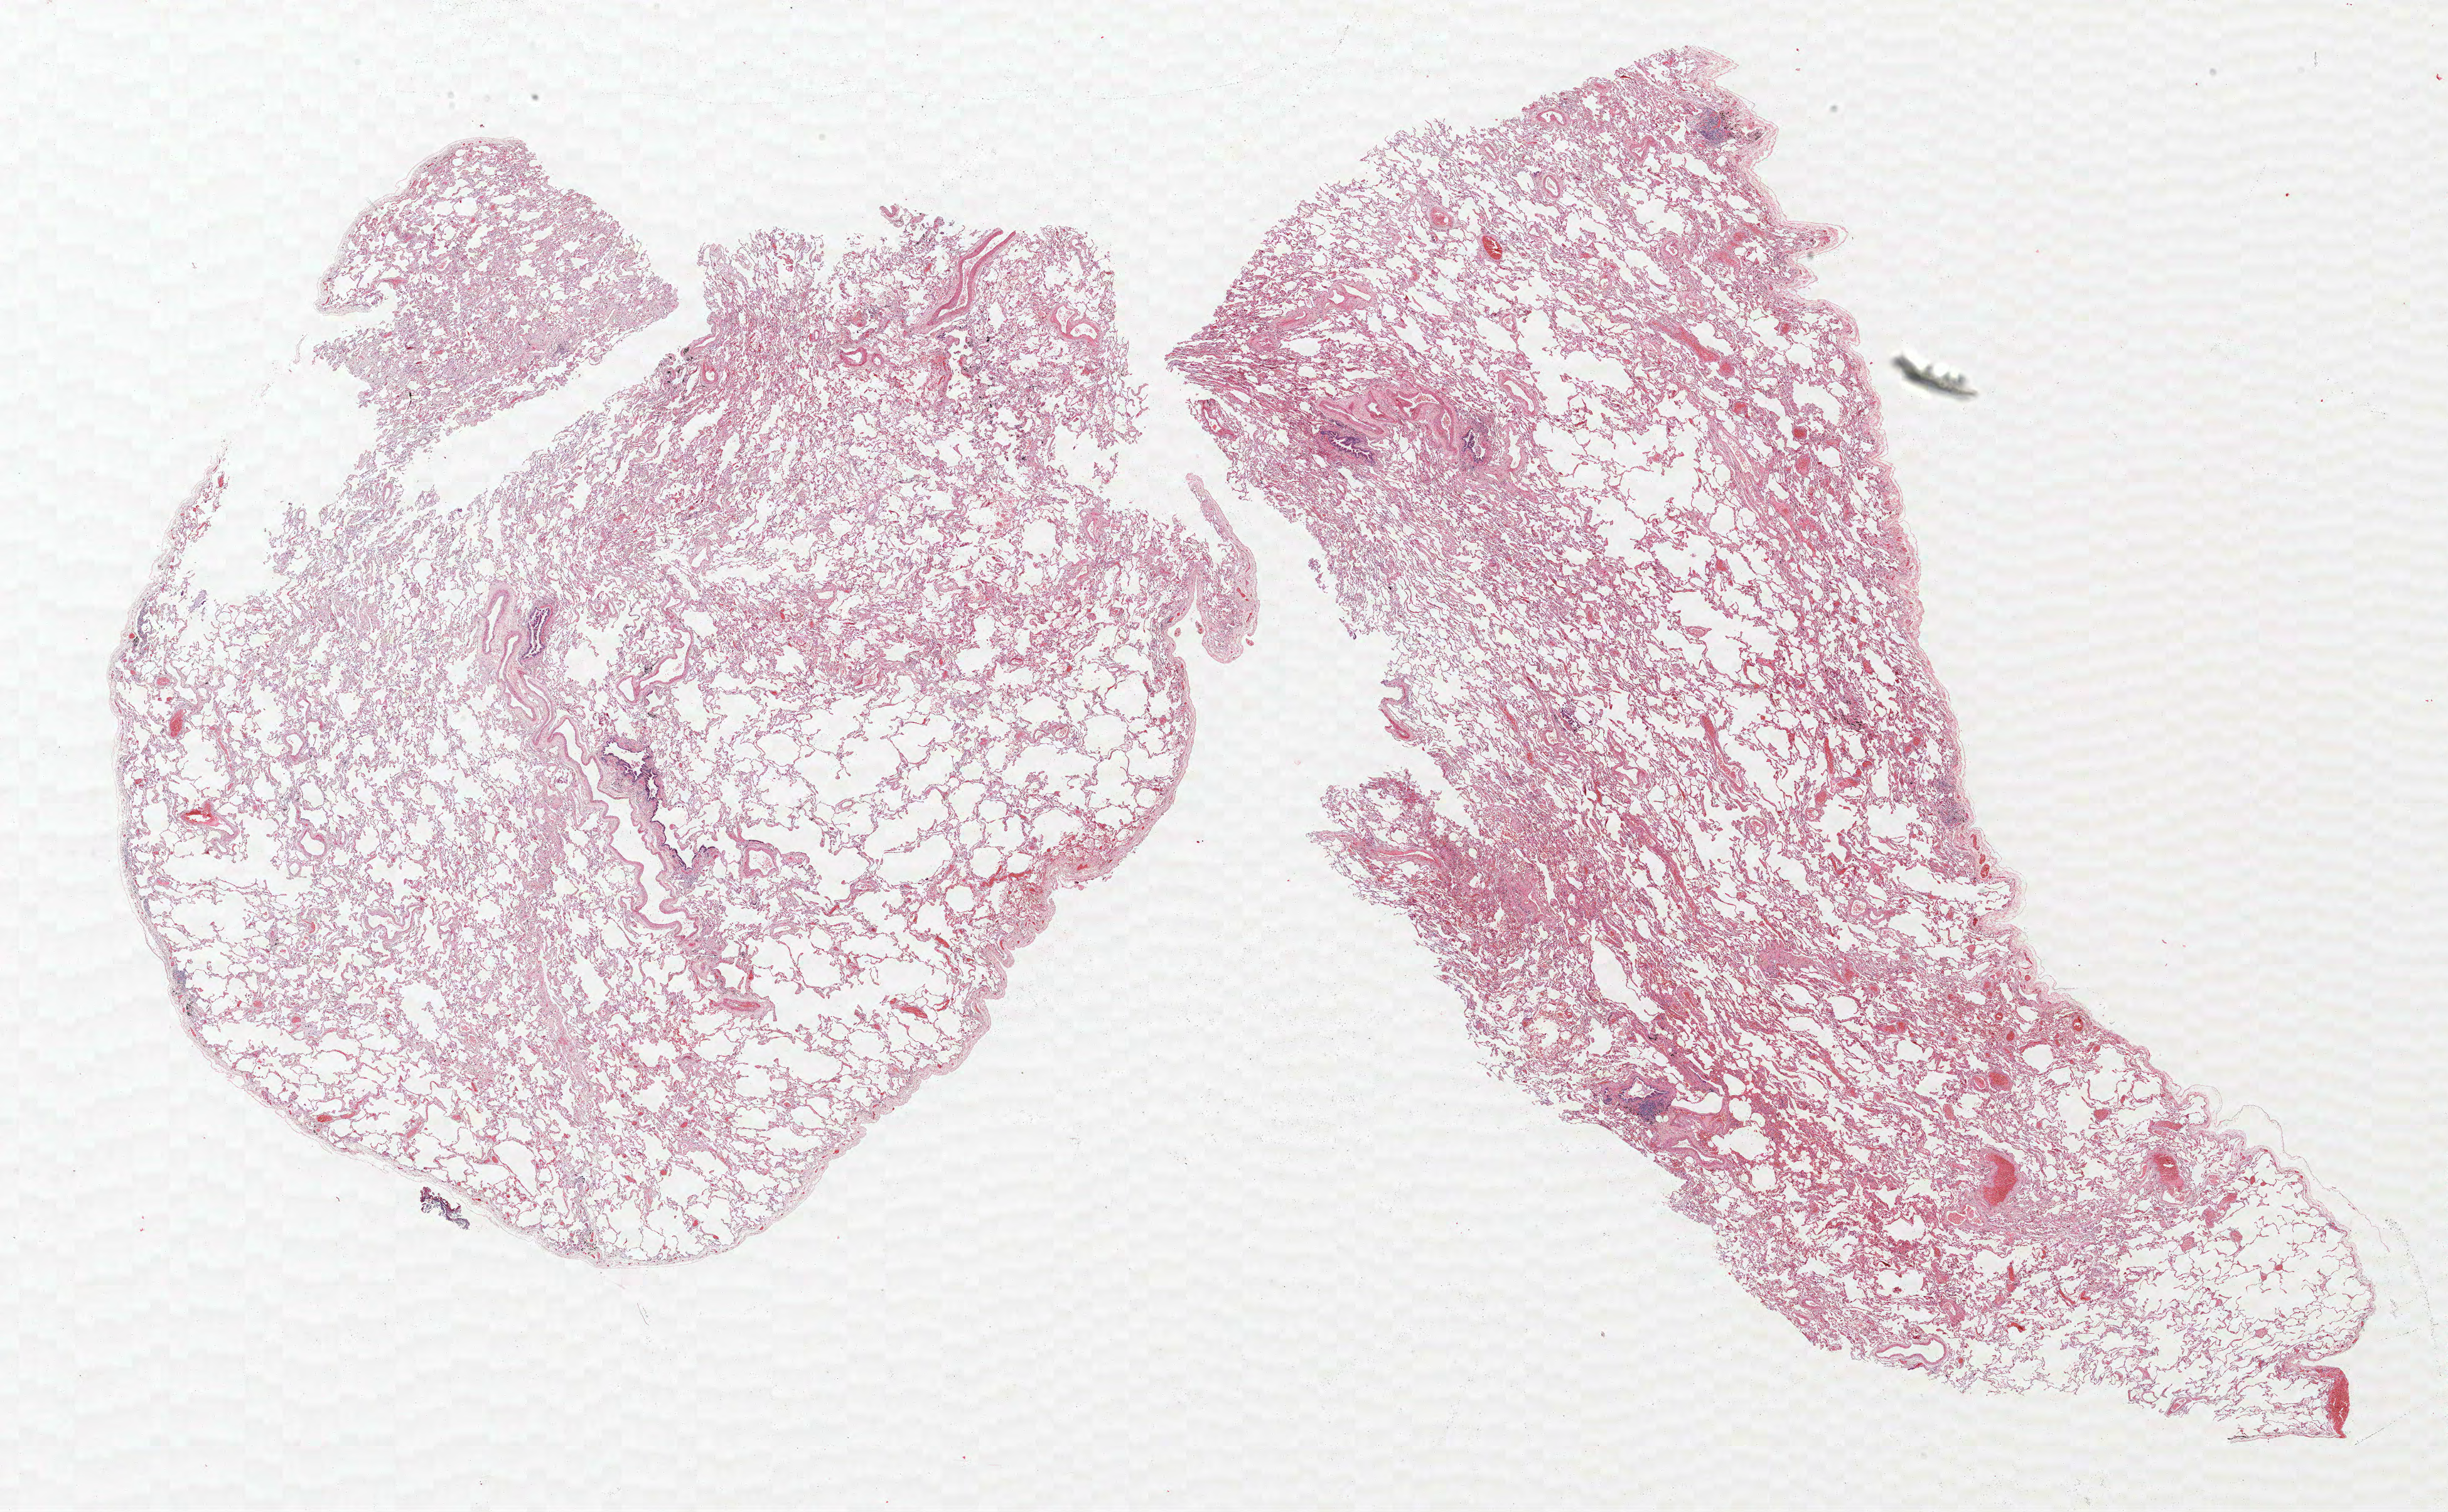
H&E whole-slide image, shown as a low-resolution overview of the whole scanned area (about 31.2 x 19.3 mm); FFPE section; lung tissue. Female patient, aged 55 at enrolment. Former smoker at enrolment.
Participant's lung-cancer diagnosis: Bronchiolo-alveolar adenocarcinoma, NOS.